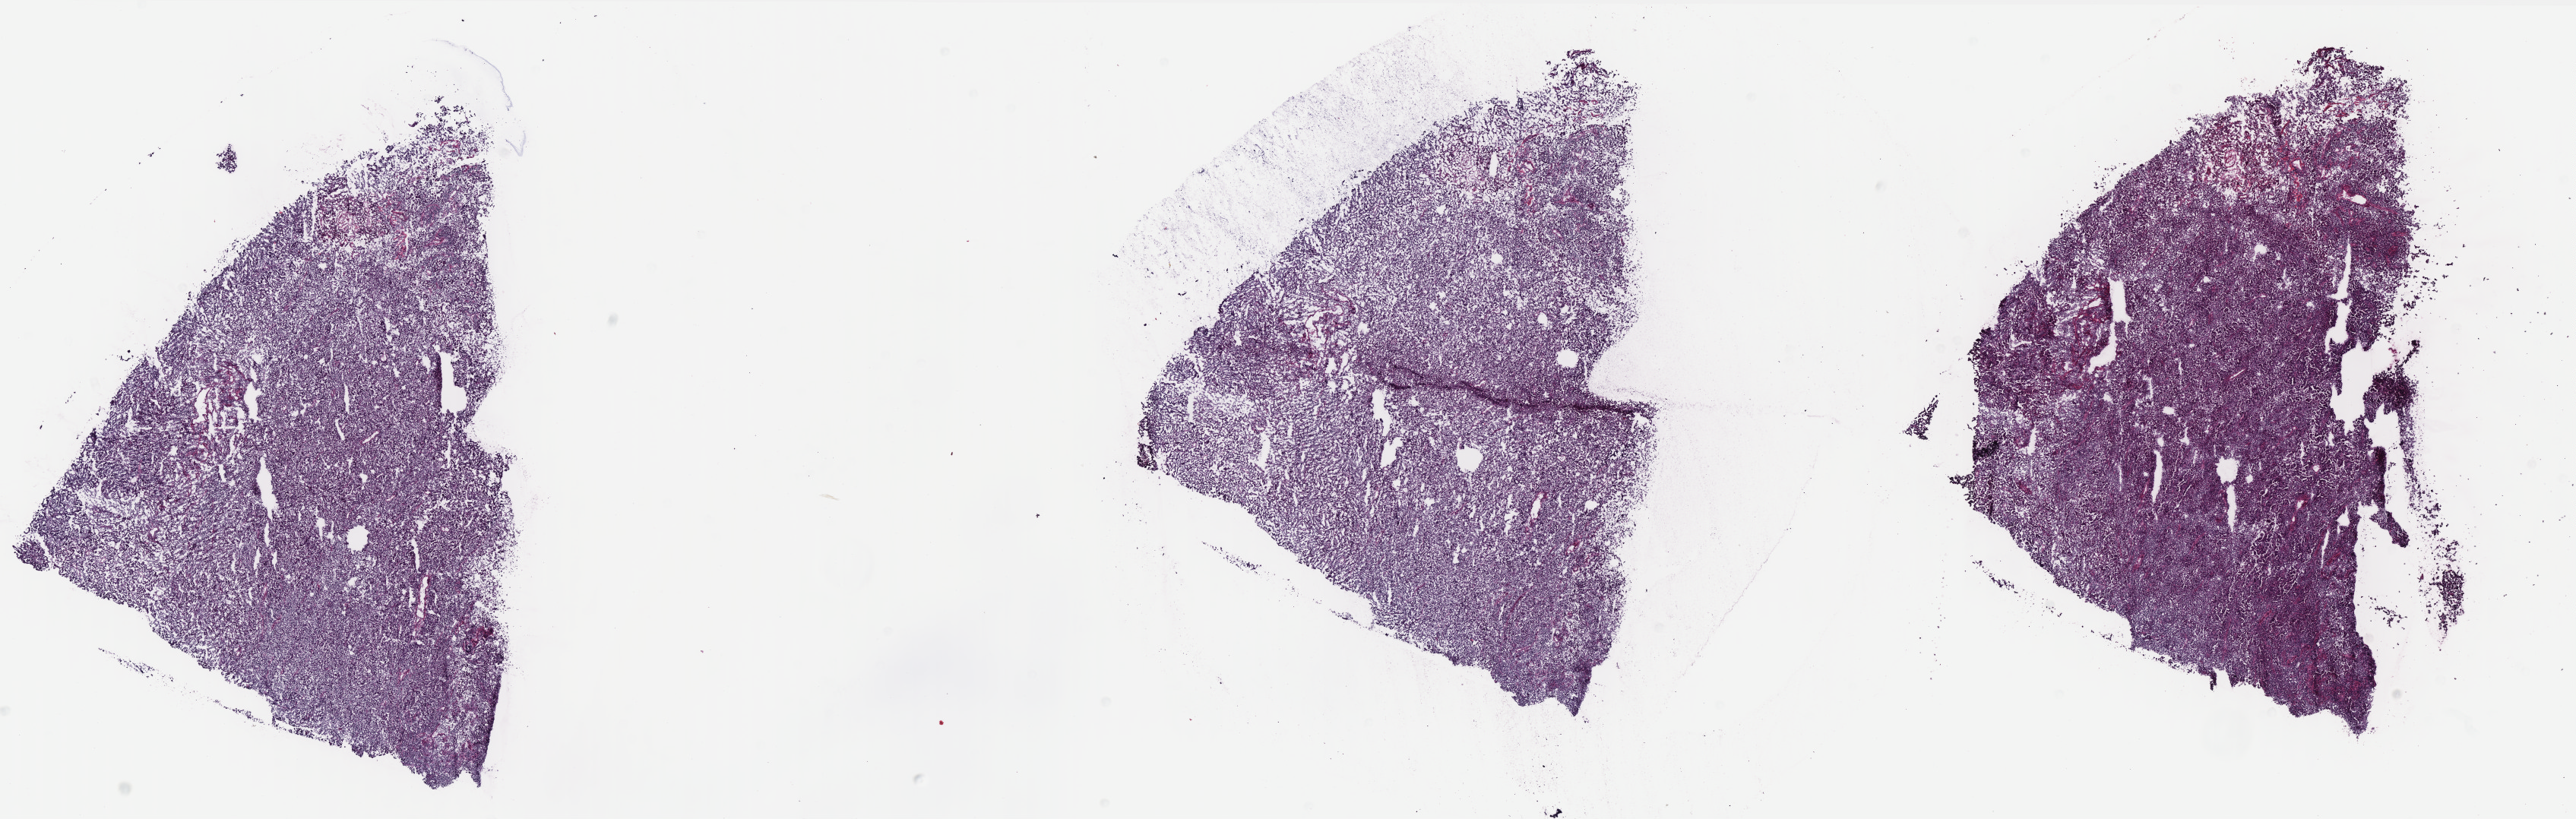
H&E whole-slide image, low-resolution overview of the scanned area, about 27.2 x 8.6 mm. Frozen section from the bottom of the tissue portion. Primary tumour sample from the uterus. Female, age 67 years at initial diagnosis. Histologic grade: G3 (poorly differentiated). Slide review estimates, as recorded: tumour cells 60%, tumour nuclei 60%, normal cells 10%, stromal cells 25%, necrosis 5%. Infiltration values recorded for this section: lymphocyte infiltration 90%, monocyte infiltration 0%, neutrophil infiltration 0%.
• histologic diagnosis: Serous cystadenocarcinoma, NOS (endometrium)
• FIGO stage: IA
• lymph nodes positive (case pathology): 0 of 10 examined